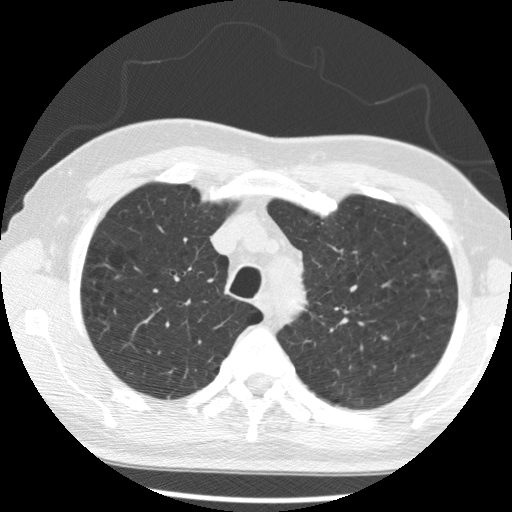
Low-dose screening chest CT, axial slice, second annual screen, lung window (W 1500 / L -600 HU), 2.5 mm slice thickness, standard (soft-tissue) reconstruction kernel (STANDARD), 120 kVp, slice 66 of 285 in the series. Male participant, aged 68 years at enrolment. Current smoker at enrolment.
- Expert reader's lesion annotation, bounding box <413,258,460,294> (left, top, right, bottom; pixels).
- Screening reader's record for this exam (one nodule recorded; not confirmed to be the boxed lesion): non-calcified nodule or mass ≥4 mm, left upper lobe, 15 × 11 mm, poorly defined margins, ground glass attenuation, pre-existing on the prior screen: yes; interval growth: yes.
- Official screen result: positive, change unspecified: nodule(s) >= 4 mm or enlarging nodule(s), mass(es), or other non-specific abnormalities suspicious for lung cancer.